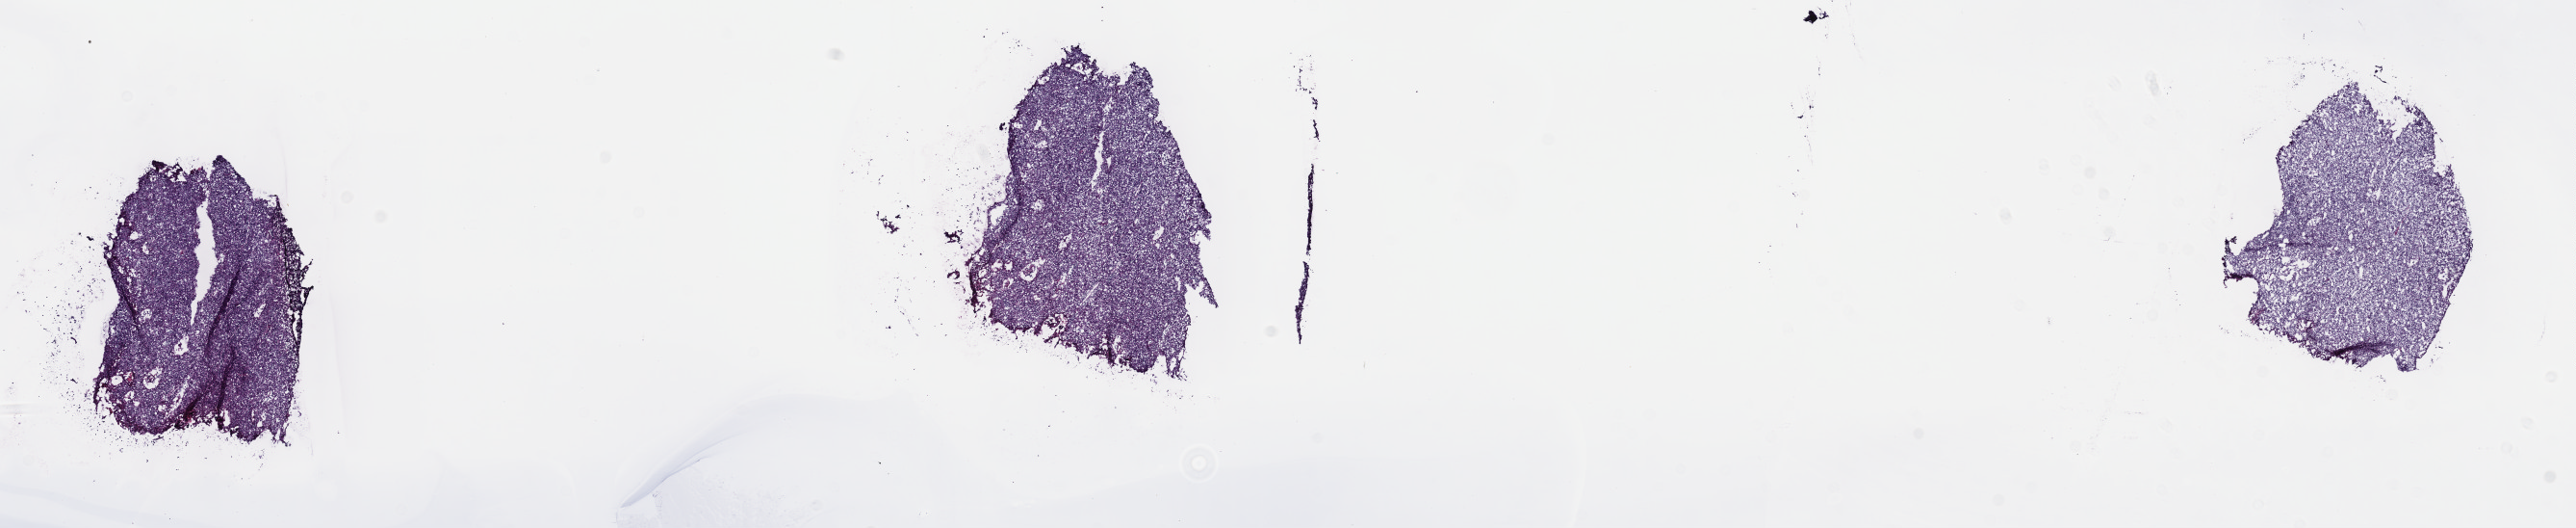
Whole-slide histology image, H&E, a low-resolution overview of the entire scanned area, about 21.6 x 4.4 mm (slide scanned at 40x), frozen section from the top of the tissue portion, sample: primary tumour, thymus. Female patient; age at initial diagnosis 71 years. Pathologist review of this section (percent, as recorded): tumour cells 100%, tumour nuclei 80%, normal cells 0%, stromal cells 0%, necrosis 0%. Infiltration values recorded for this section: lymphocyte infiltration 1%, monocyte infiltration 0%, neutrophil infiltration 0%.
Pathologic diagnosis: Thymoma, type B3, malignant.